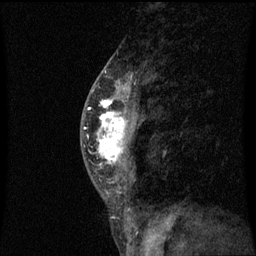
Breast MRI (dynamic contrast-enhanced), one sagittal slice; slice 31 of 60 in the series (ordered by position); dynamic contrast-enhanced series, image 2 of 3 at this slice position (ordered by acquisition); 1.5 T; TE 4.2 ms, TR 8.9 ms; 2 mm slice thickness; 256 × 256 image matrix. Female patient, age 50 years. Case-level facts recorded for this patient, not image findings: setting: breast cancer imaged before/during neoadjuvant chemotherapy; receptor status: triple-negative.
Annotated regions visible in this slice (semi-automatically segmented with operator editing):
- analysis volume of interest (the breast-tissue region the enhancement analysis was run in; not a lesion): box from (x=84, y=80) to (x=145, y=171) px
- tumour enhancement mask (voxels above the 70 % enhancement threshold inside the analysis volume of interest): (x=84, y=84)–(x=131, y=165)